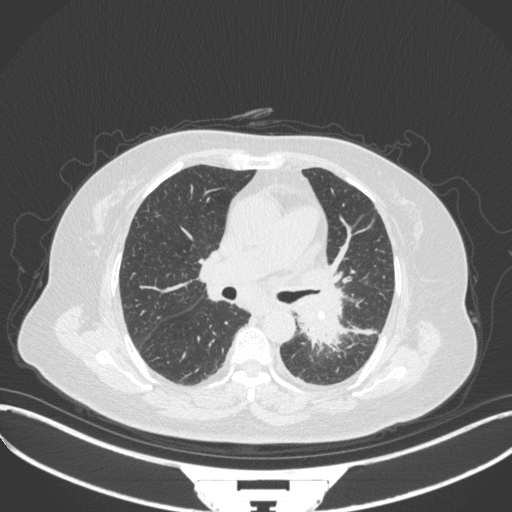
Chest CT, one axial slice; position 201 of 328 along the scan axis; 120 kVp; lung window (W 1500 / L -600 HU); 512 × 512 image matrix, field of view 400 × 400 mm. Female patient, age 69 years. From the clinical record (not read from this slice): clinical TNM (as recorded): T2b N3 M1.
Outlined on this slice (bounding box drawn by a radiologist):
- lung tumour (recorded histology: adenocarcinoma): box from (x=292, y=289) to (x=348, y=350) px